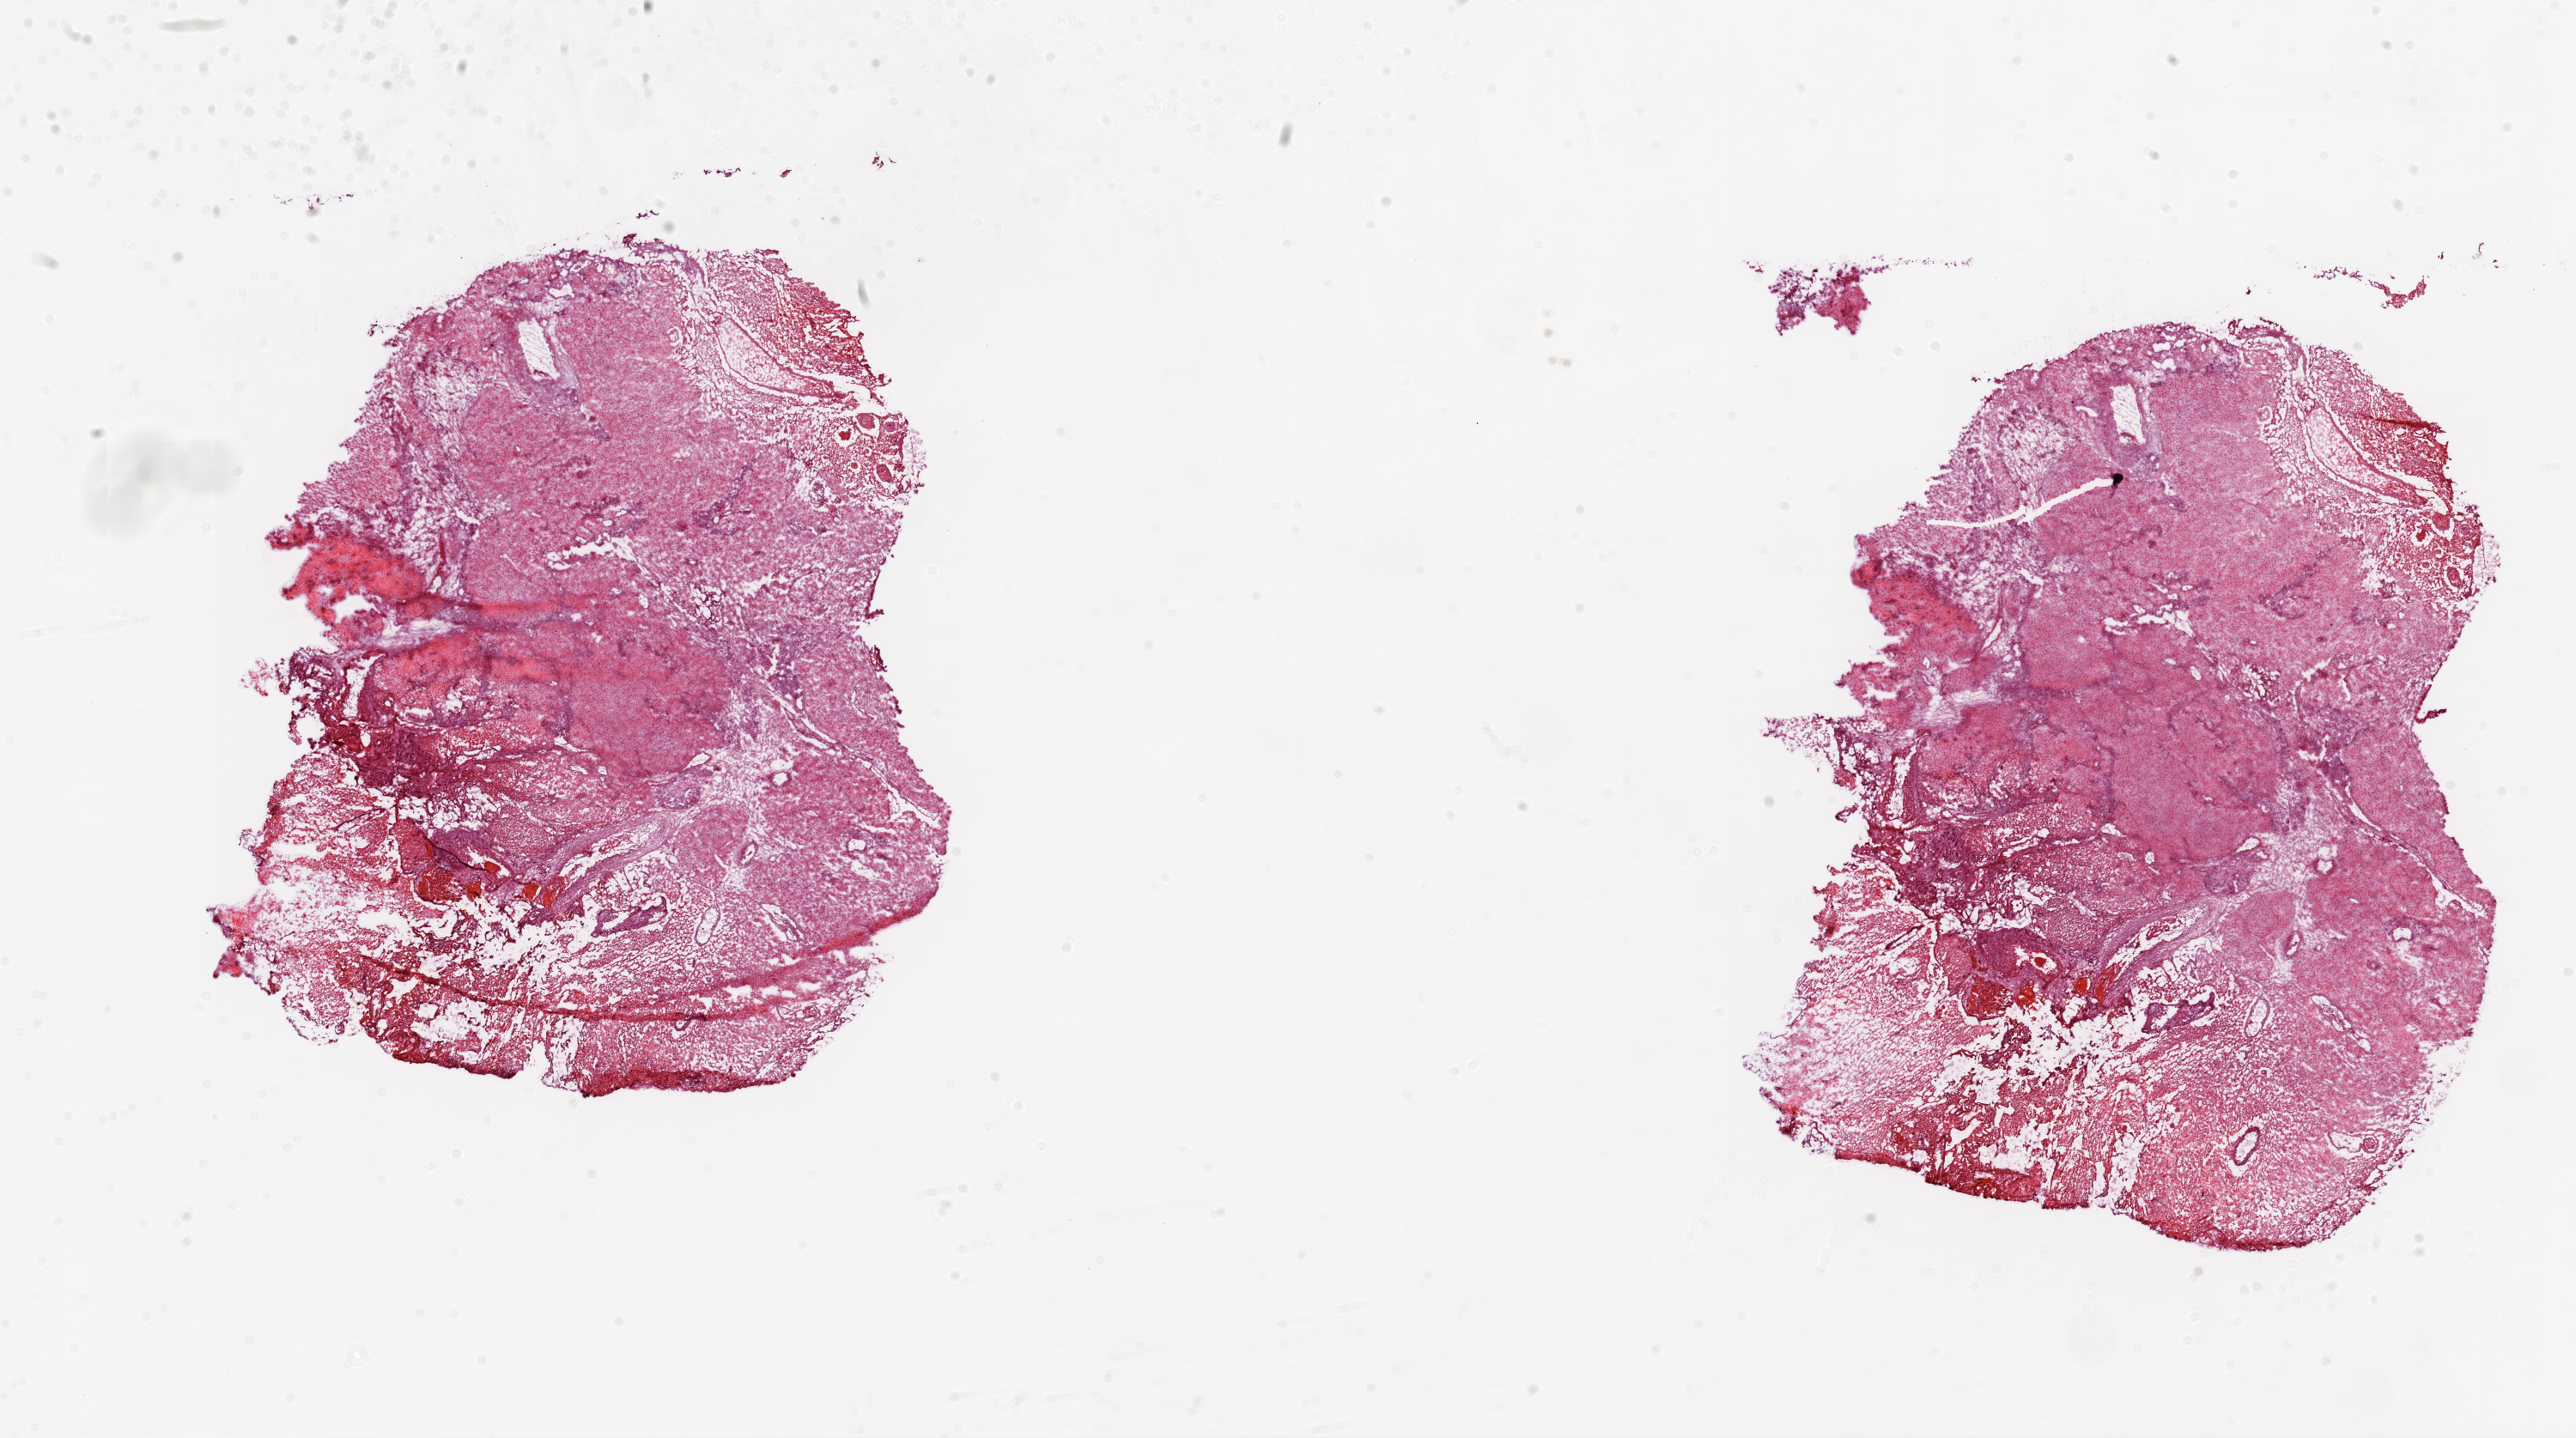
H&E-stained whole-slide image — a low-resolution overview of the entire scanned area, about 24.1 x 13.4 mm; frozen section from the top of the tissue portion; sample: primary tumour, brain. Male, age 62 years at initial diagnosis. Slide review estimates, as recorded: tumour cells 82%, tumour nuclei 85%, normal cells 0%, stromal cells 3%, necrosis 15%.
* histologic diagnosis: Glioblastoma